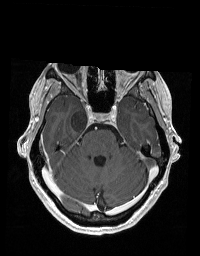
Brain MRI from a brain-tumour surgery series, one axial slice; slice 128 of 192 in the series (ordered by position); T1-weighted post-contrast; 200 × 256 image matrix, field of view 195 × 250 mm. From the clinical record (not read from this slice): histopathology: Glioblastoma; WHO grade: 2; IDH mutation: no.
Annotated regions visible in this slice (outlined manually by an expert reader):
- tumour: bounding box (x1, y1, x2, y2) in pixels: (71, 109, 88, 132)